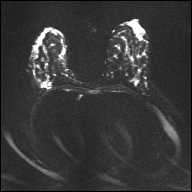
Breast MRI, one axial slice; position 17 of 32 along the scan axis; diffusion-weighted series; image 2 of 4 stored at this slice position (different b-values; order by instance number); 1.5 T; 192 × 192 image matrix, field of view 360 × 360 mm. Female patient.
Structures marked on this image (manually delineated by an expert):
- tumour on diffusion-weighted imaging: box from (x=41, y=82) to (x=48, y=86) px